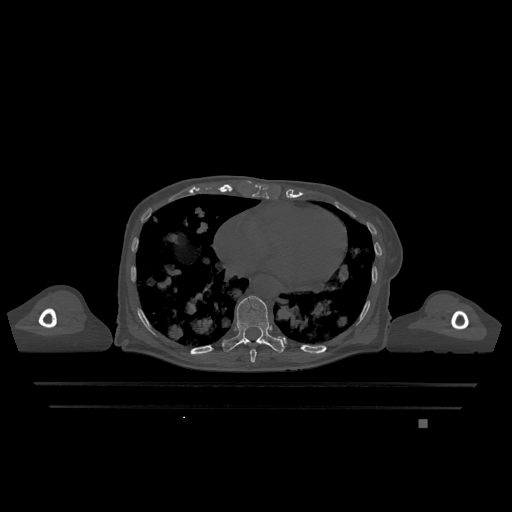
CT including the spine, one axial slice. Slice 655 of 1317 in the series (ordered by position). Bone window (W 1800 / L 400 HU). 0.5 mm slice thickness. 512 × 512 image matrix, field of view 500 × 500 mm. Female patient, age 74 years. Case-level facts recorded for this patient, not image findings: primary cancer: lung.
Outlined on this slice (semi-automatic segmentation, software-assisted and operator-edited):
- T10 vertebra: box from (x=222, y=296) to (x=285, y=353) px
- T9 vertebra: (x=250, y=349)–(x=257, y=363)